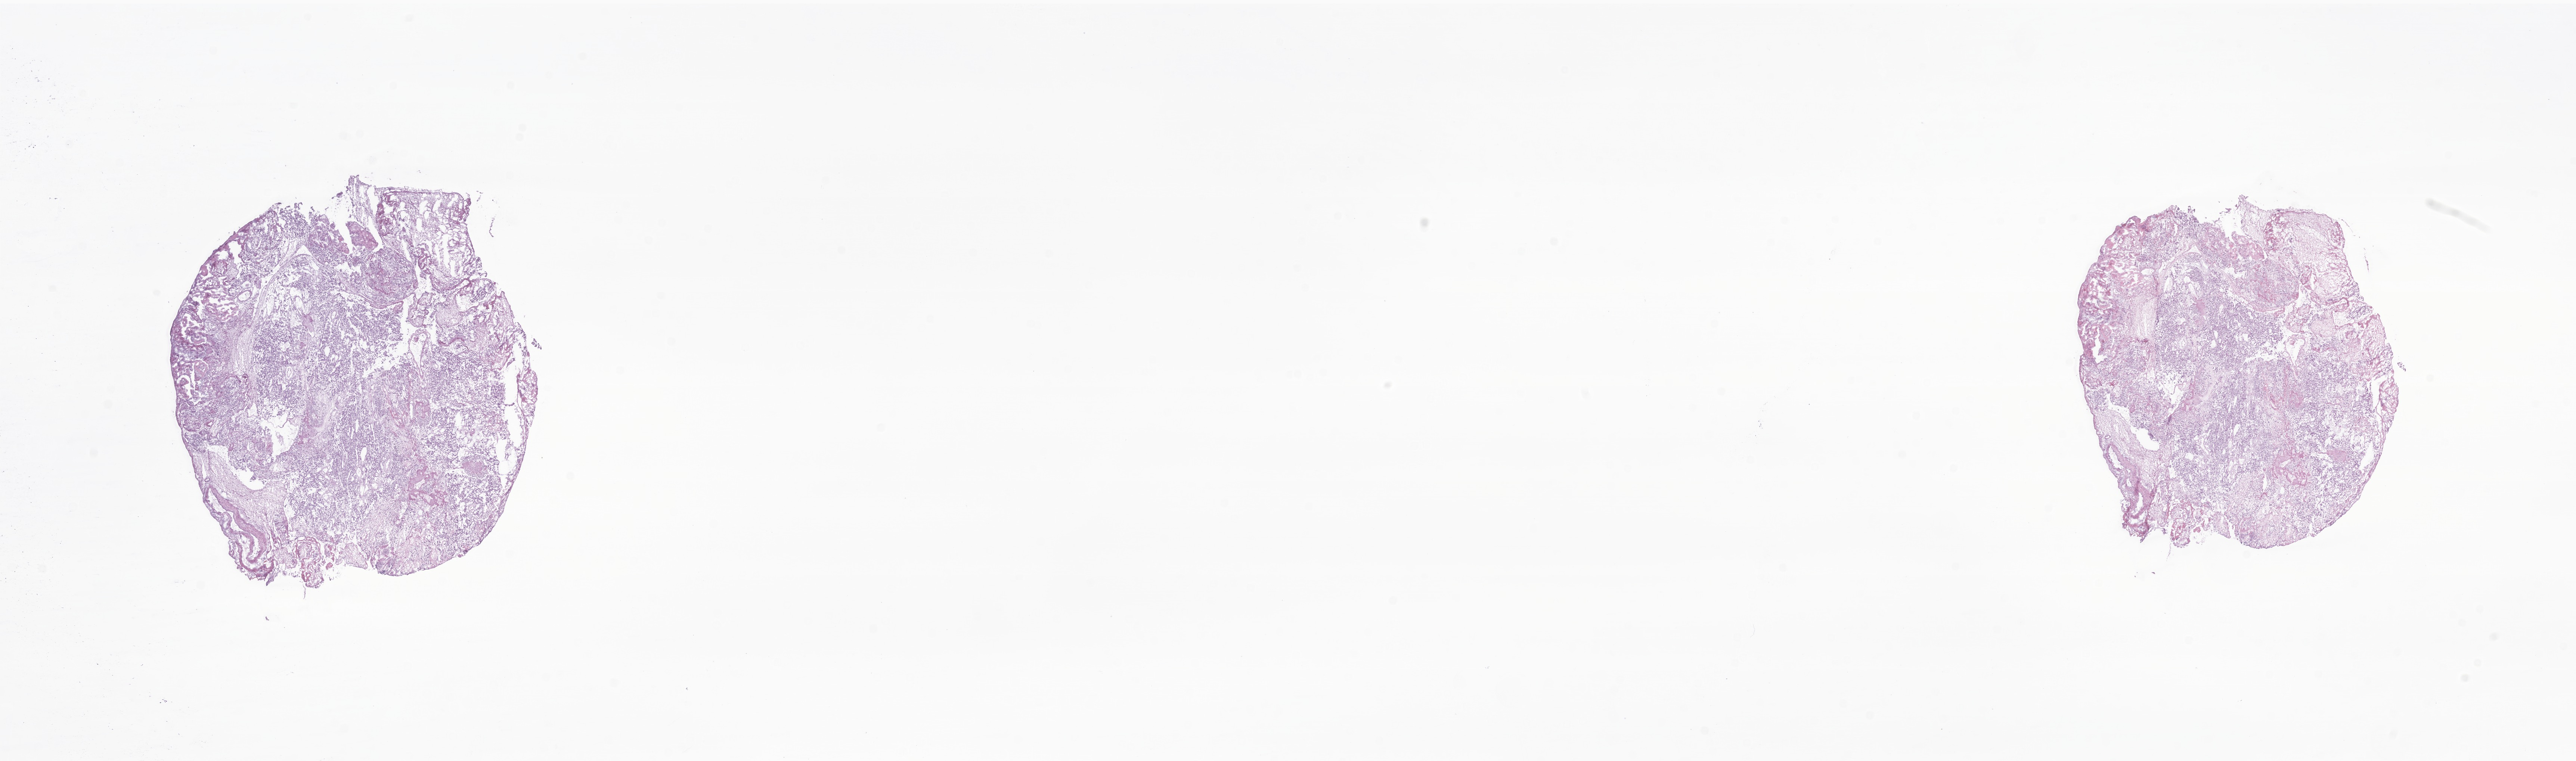
Haematoxylin and eosin whole-slide image of tumor tissue from the spinal cord — whole scanned area (about 29.1 x 8.6 mm) shown as a low-resolution overview. Frozen section. Male patient, age 123 months (10 years 3 months).
Diagnosis (ICD-O-3 morphology term): Myxopapillary ependymoma.